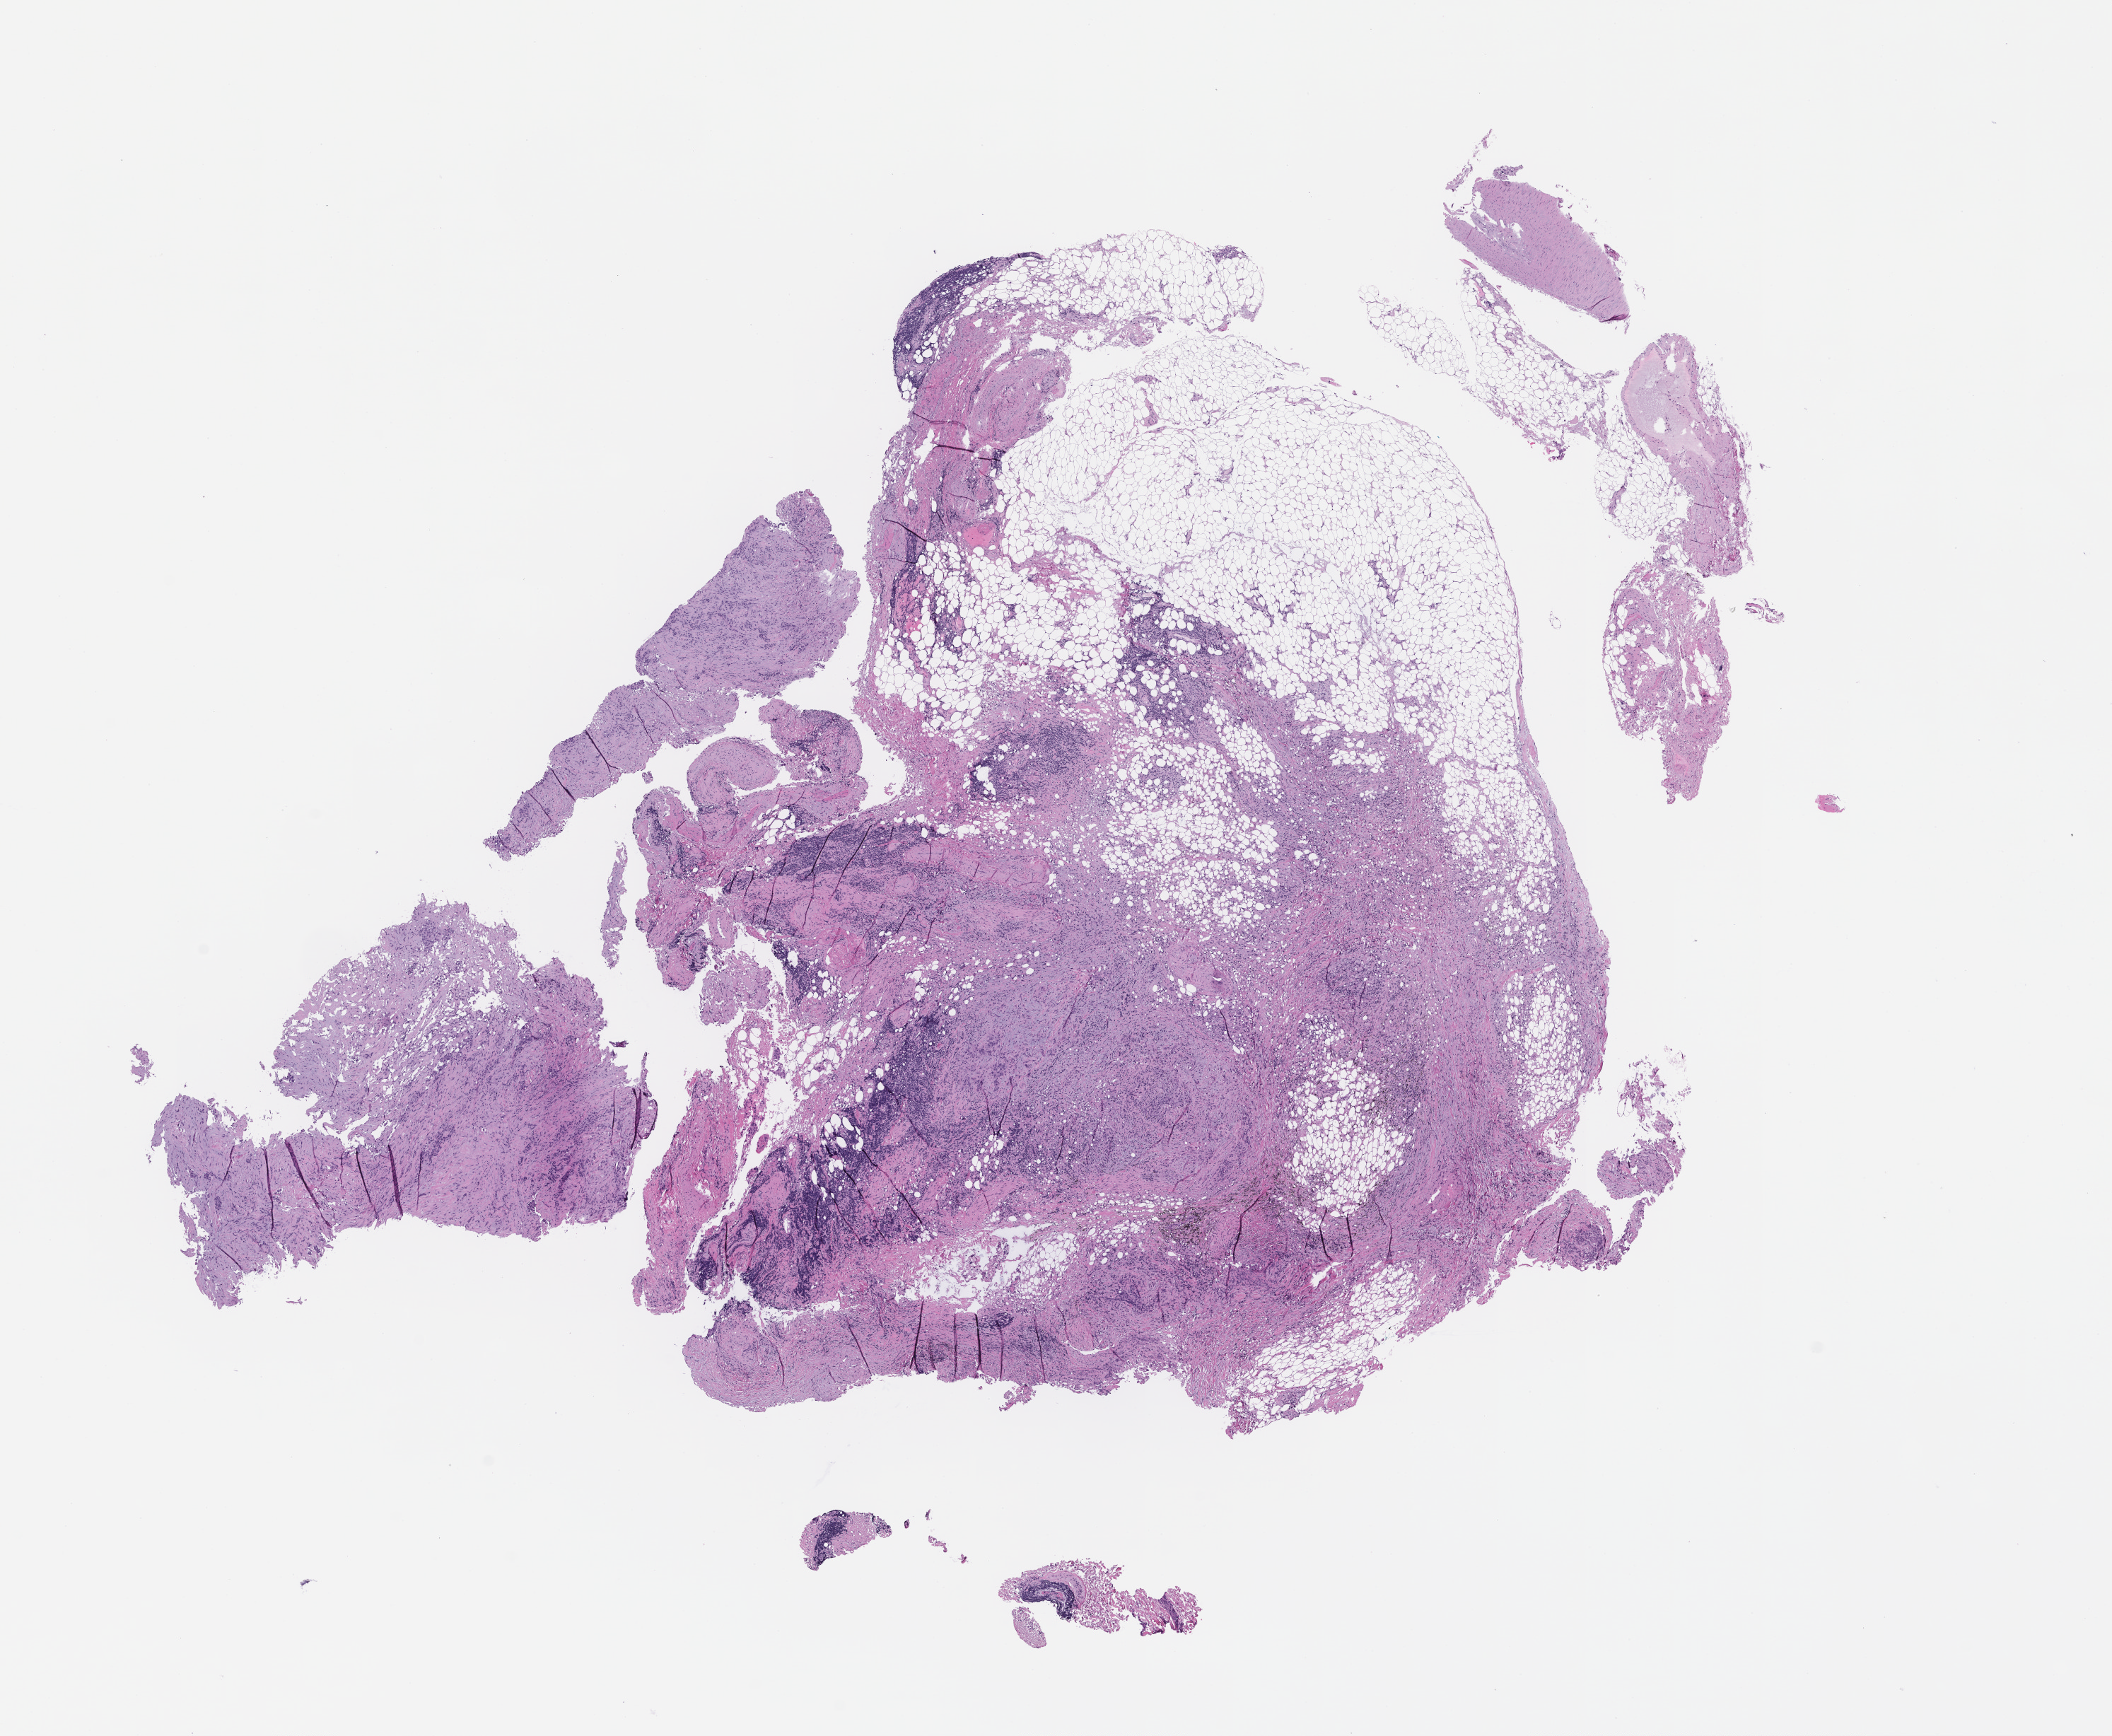
Whole-slide image, H&E stain — low-resolution overview of the scanned area, about 12.1 x 9.9 mm; formalin-fixed, paraffin-embedded (FFPE) tissue; tissue site: lung; archival tissue. Patient: male.
This section: primary tumour tissue. Diagnosis: Non-Small Cell Lung Carcinoma.